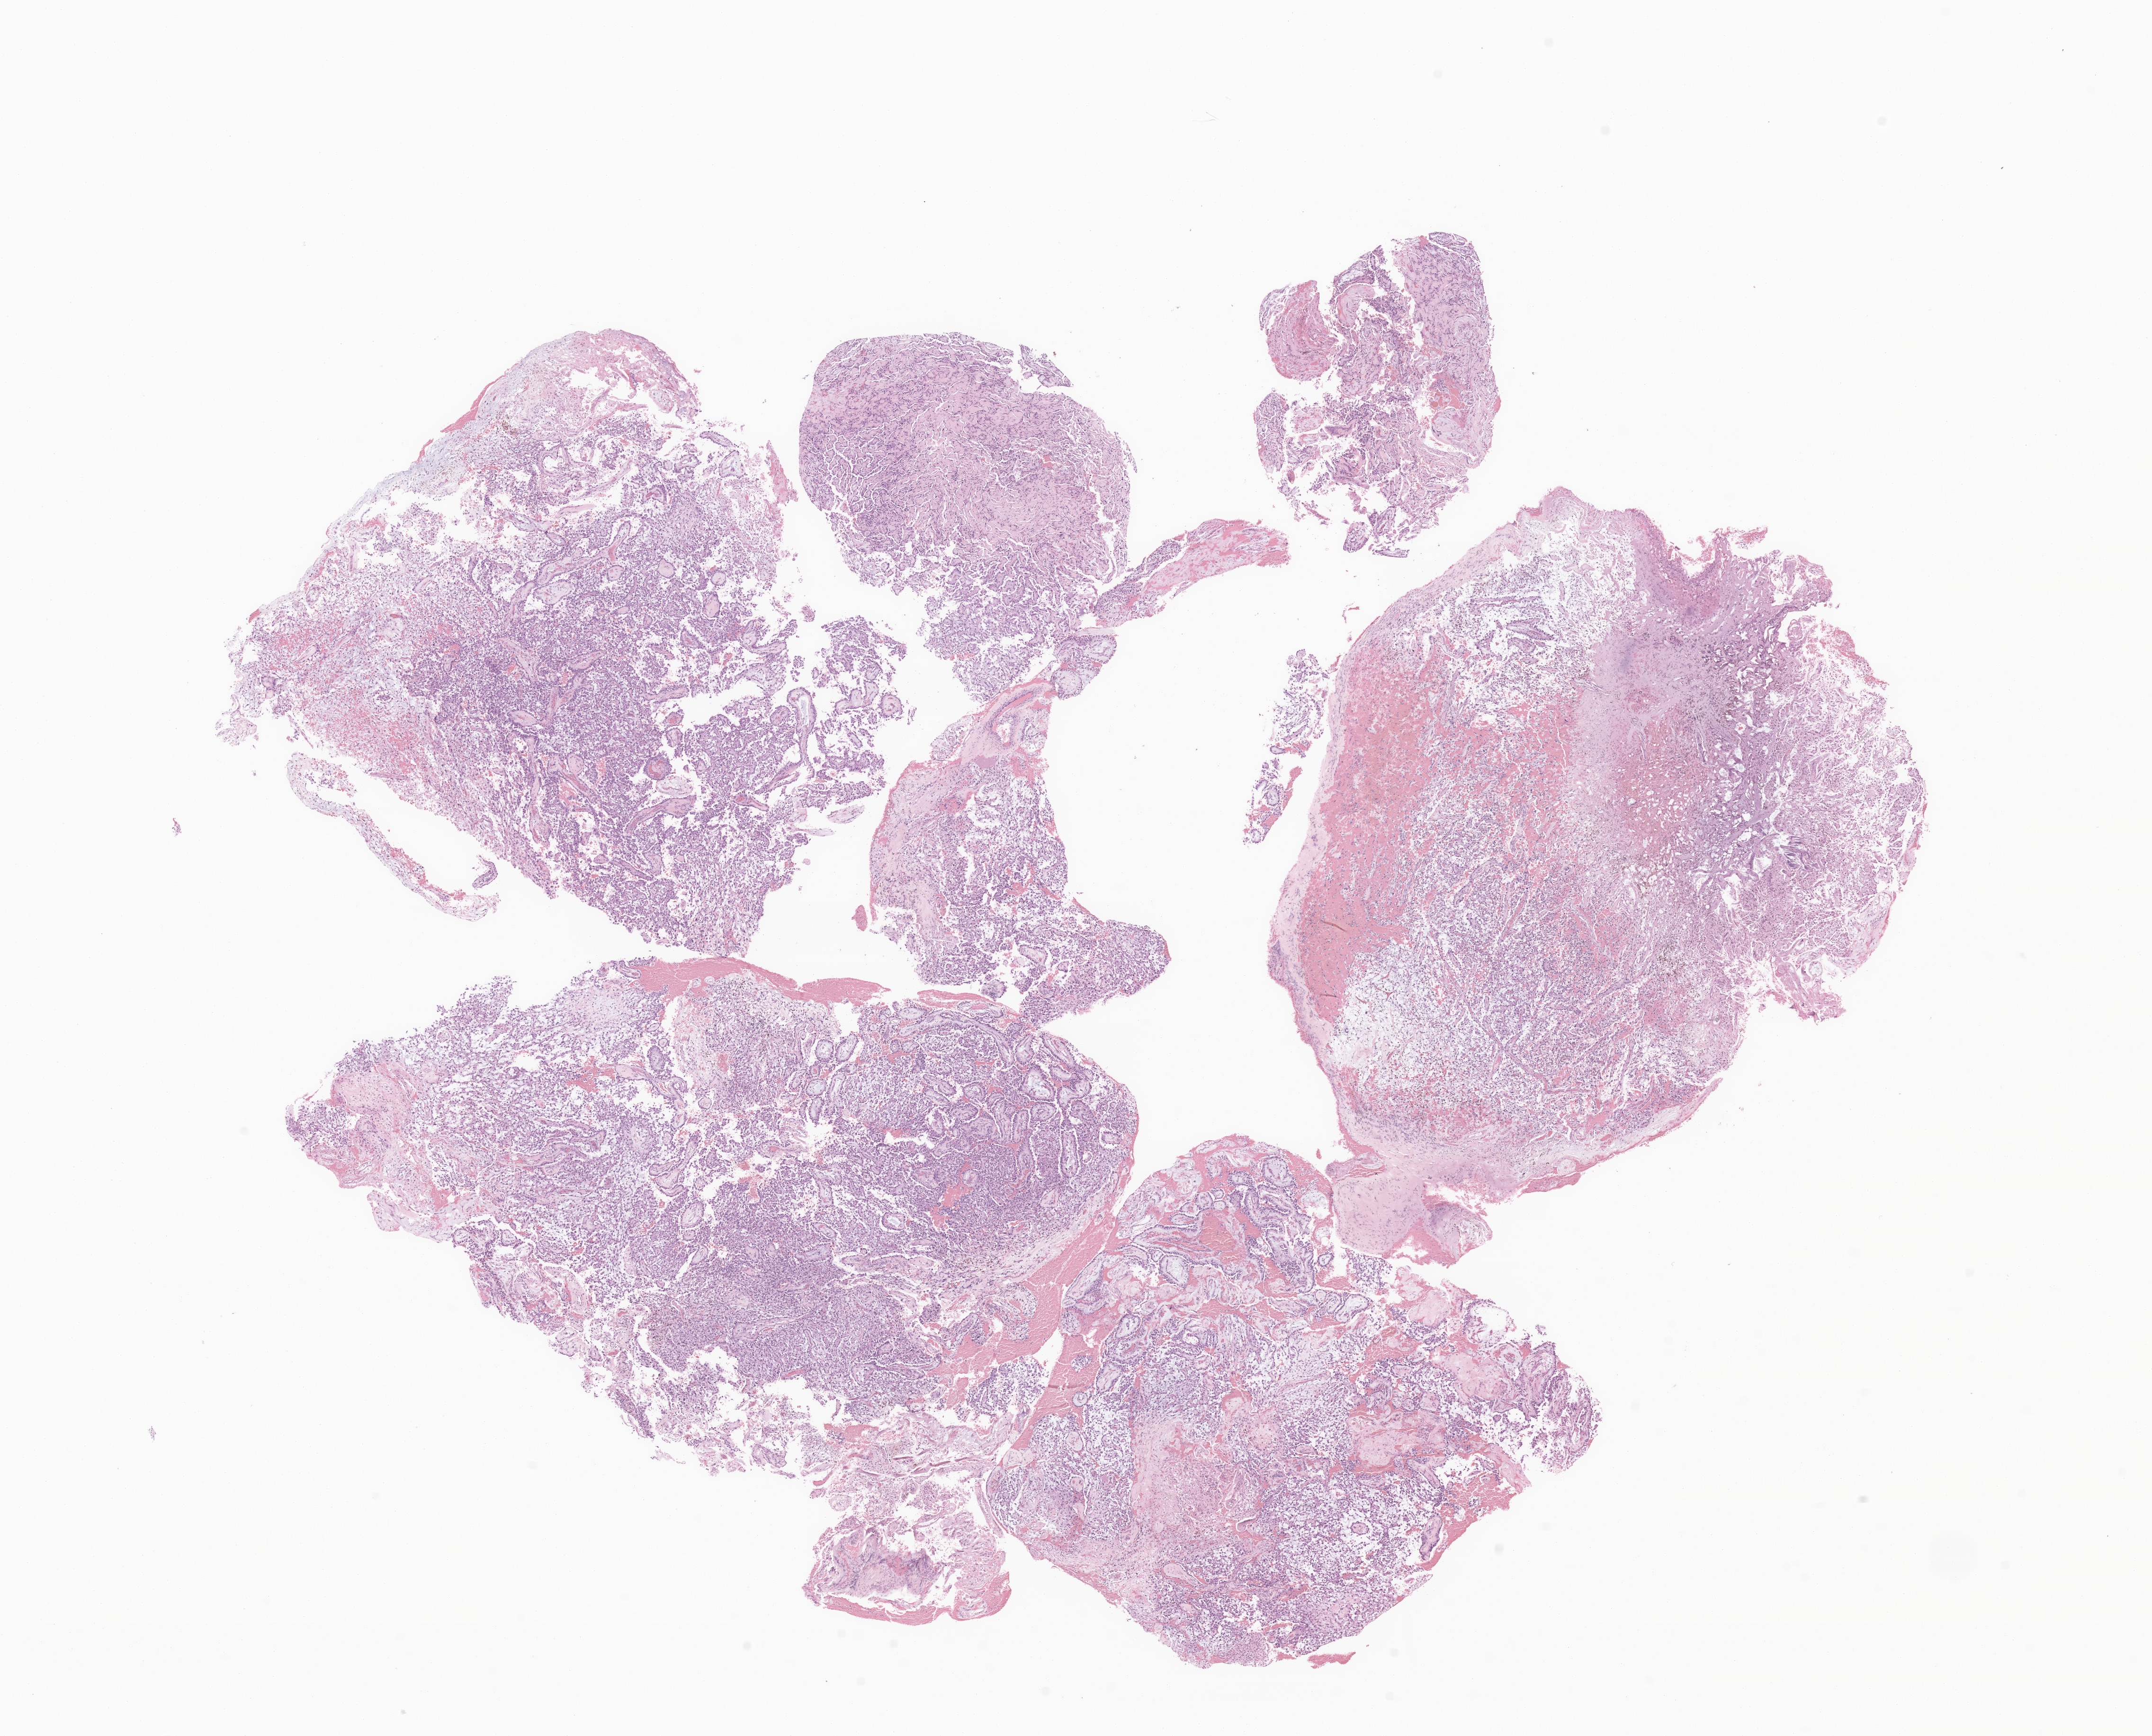
Digitized haematoxylin and eosin-stained section of tumor tissue from the spinal cord — a low-resolution overview of the entire scanned area, about 19.2 x 15.5 mm. Formalin-fixed, paraffin-embedded (FFPE) tissue. Patient male; age 172 months.
Diagnosis: Myxopapillary ependymoma.